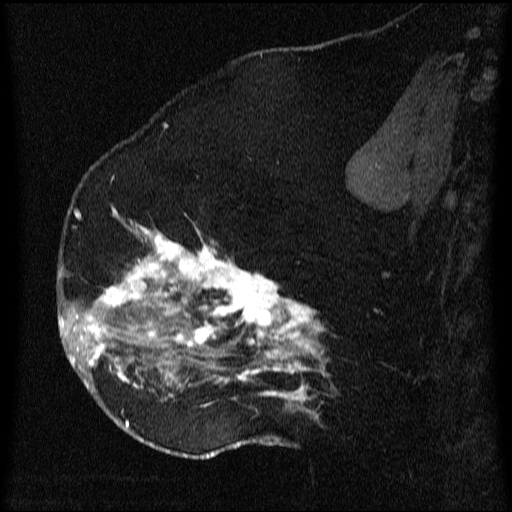
Breast MRI (dynamic contrast-enhanced), one sagittal slice. Slice 38 of 64 in the series (ordered by position). Dynamic contrast-enhanced series, image 2 of 3 at this slice position (ordered by acquisition). 1.5 T. TE 4.2 ms, TR 9.1 ms. 512 × 512 image matrix, field of view 180 × 180 mm. Female patient, age 52 years.
Structures marked on this image (semi-automatically segmented with operator editing):
- analysis volume of interest (the breast-tissue region the enhancement analysis was run in; not a lesion): box from (x=61, y=203) to (x=339, y=438) px
- tumour enhancement mask (voxels above the 70 % enhancement threshold inside the analysis volume of interest): (x=61, y=208)–(x=330, y=429)